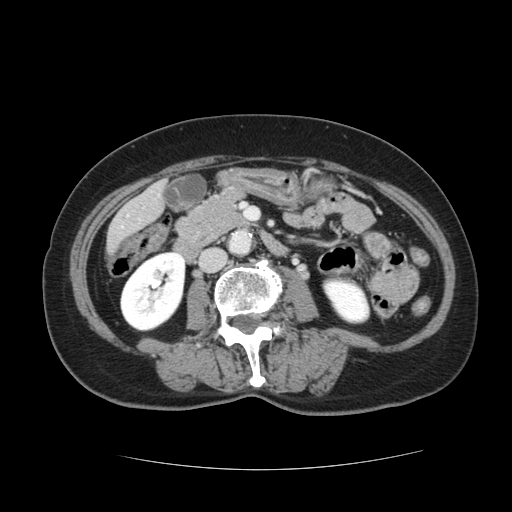
Contrast-enhanced abdominal CT, one axial slice; position 24 of 128 along the scan axis; 120 kVp; intravenous contrast given; soft-tissue window (W 400 / L 40 HU); 512 × 512 image matrix, field of view 366 × 366 mm. Female patient, age 67 years. From the clinical record (not read from this slice): diagnosis: colorectal cancer liver metastases, imaged before liver resection; multiple liver metastases: yes; largest metastasis: 3 cm; disease in both lobes: yes.
Structures marked on this image (outlined manually by an expert reader):
- liver: bounding box [x1, y1, x2, y2] px = [109, 185, 164, 248]
- planned liver remnant (the part of the liver to remain after resection): [109, 209, 141, 247]